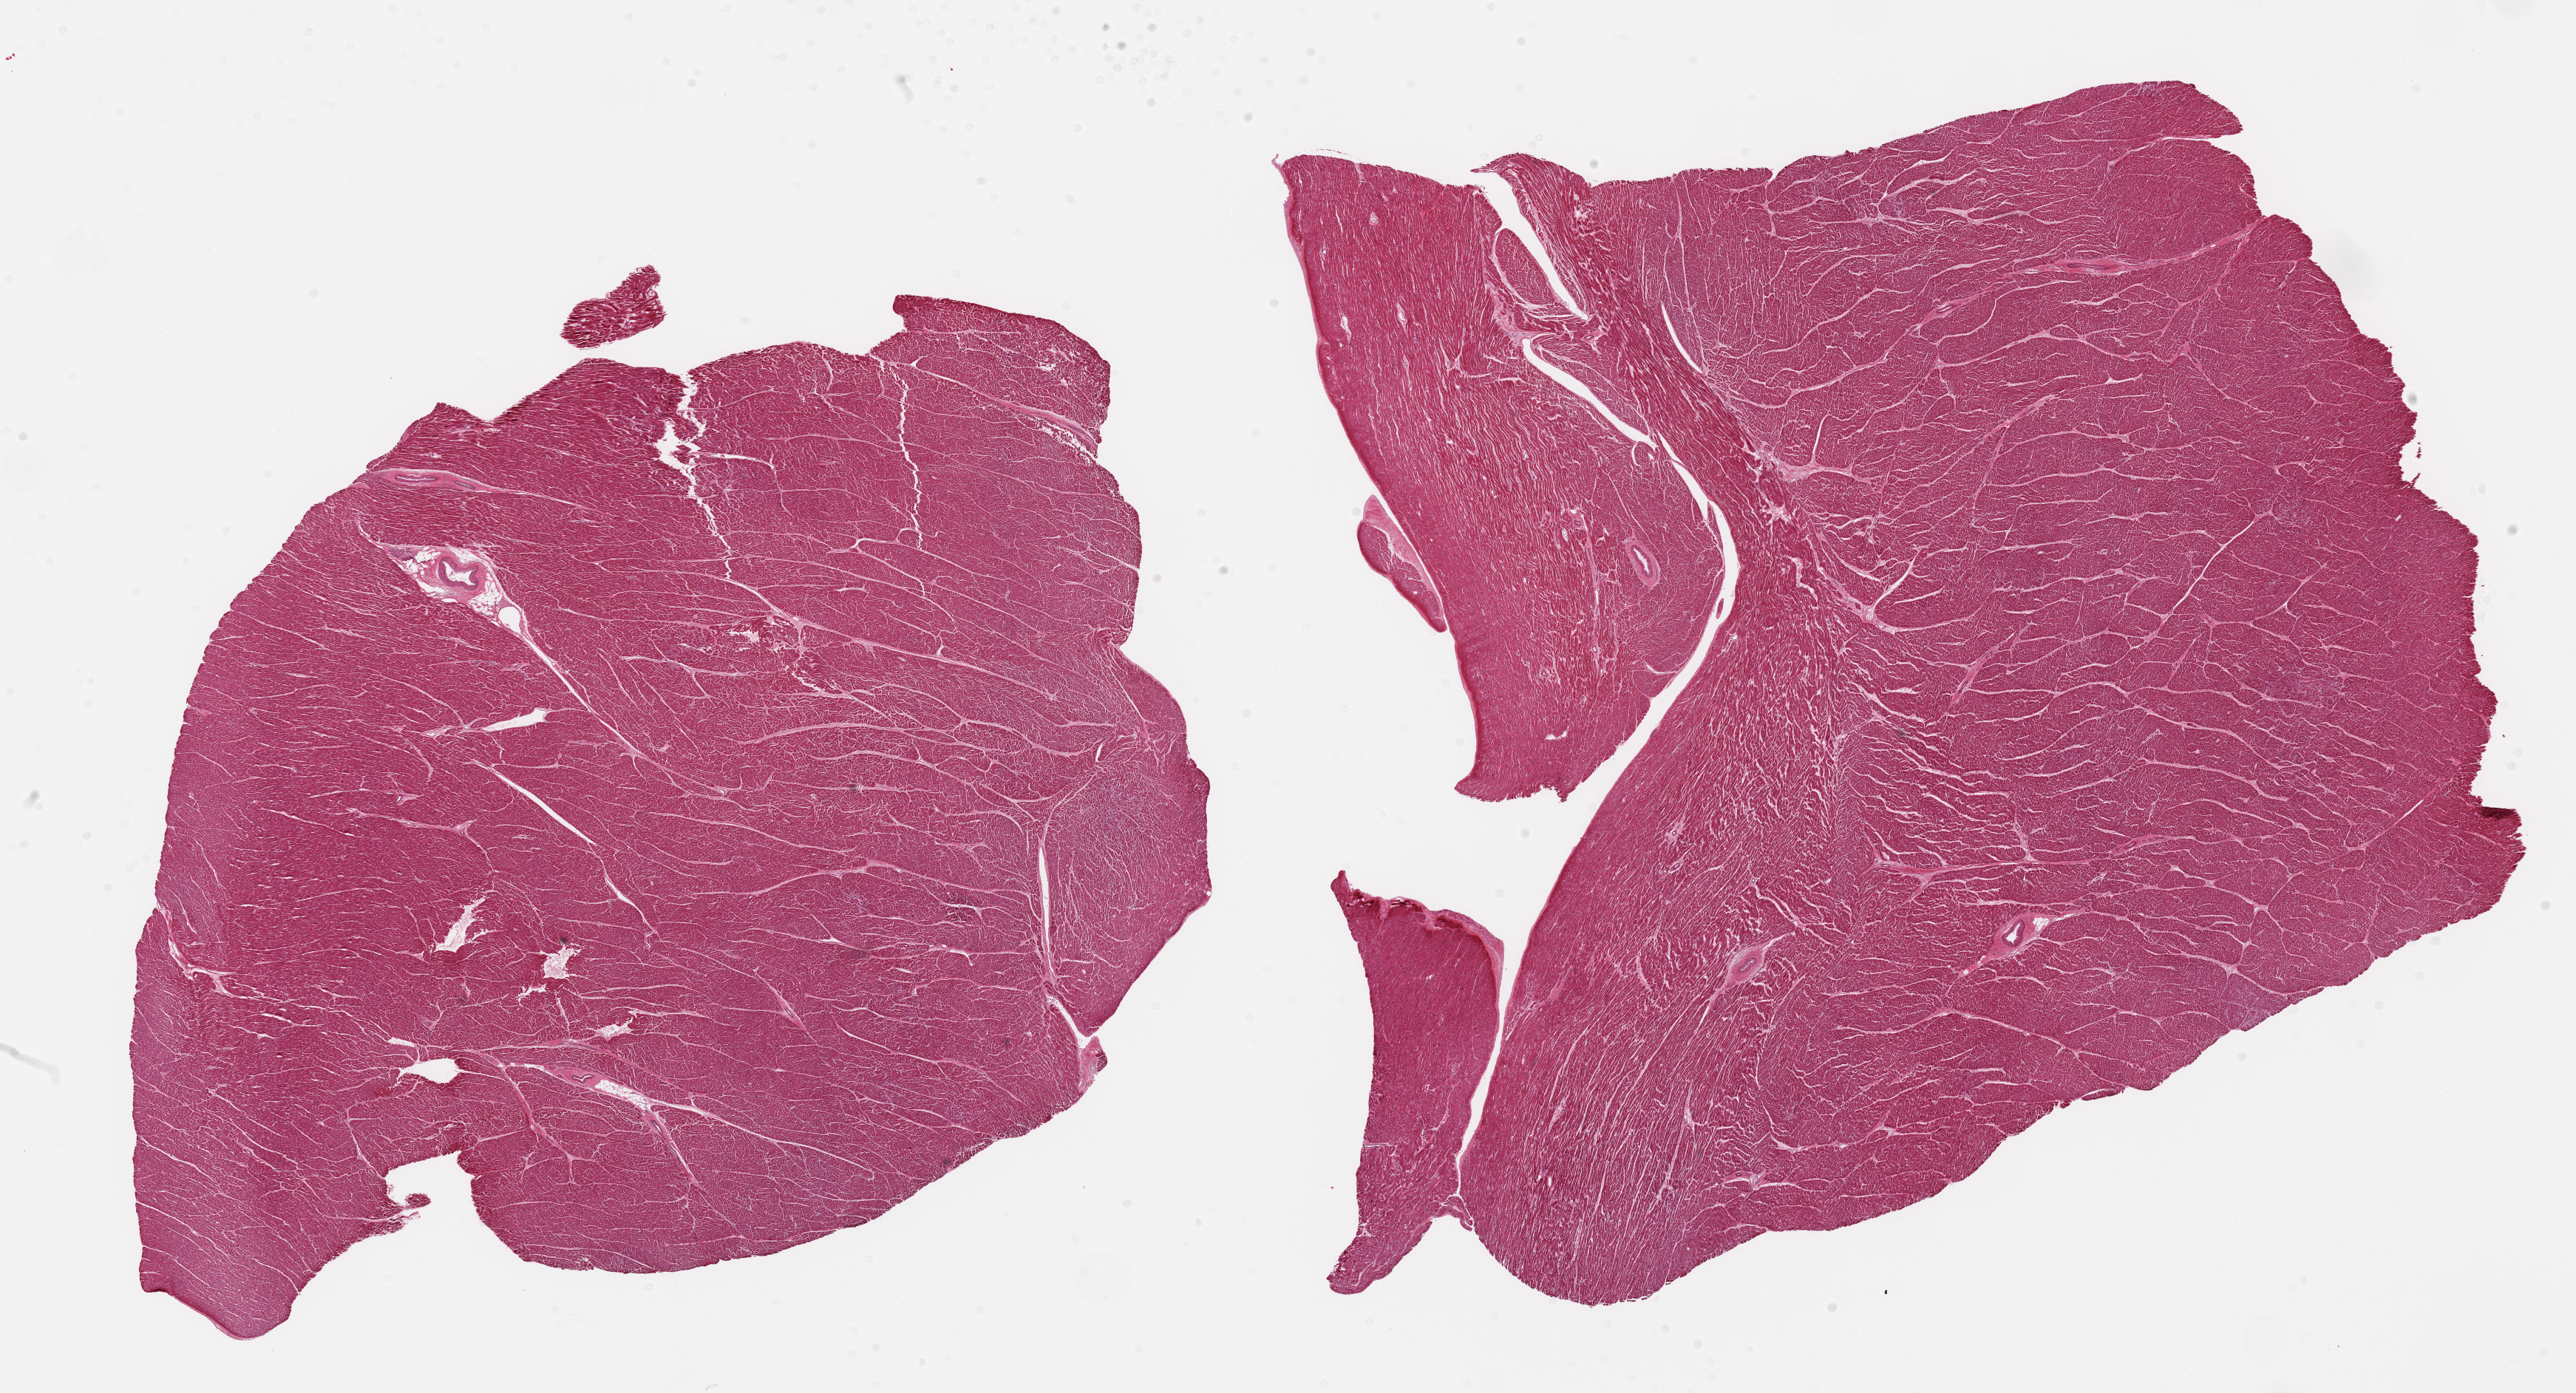
Digitized H&E-stained section, brightfield — low-resolution overview of the scanned area, about 27.6 x 14.9 mm (acquisition: 20x scan), PAXgene-fixed paraffin-embedded (PFPE) section, target tissue: heart, donor tissue sample. Donor: male.
• reviewer comment on this tissue sample: 2 pieces